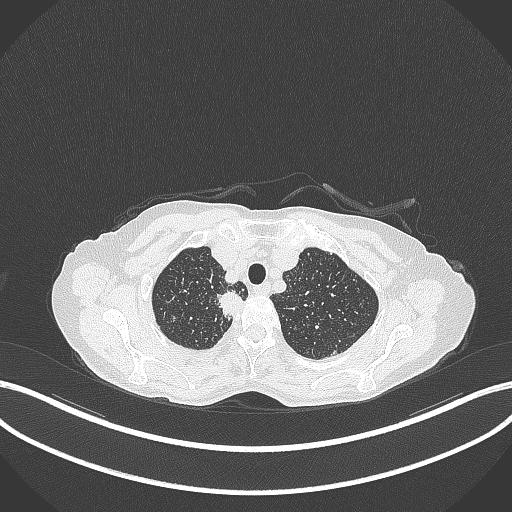
Chest CT, one axial slice; slice 319 of 403 in the series (ordered by position); 120 kVp; lung window (W 1500 / L -600 HU); 1 mm slice thickness; 512 × 512 image matrix. Patient: female, 75 years. Case-level facts recorded for this patient, not image findings: clinical TNM (as recorded): T1c N1 M1.
Outlined on this slice (bounding box drawn by a radiologist):
- lung tumour (recorded histology: adenocarcinoma): bounding box <214,286,247,320> (left, top, right, bottom; pixels)